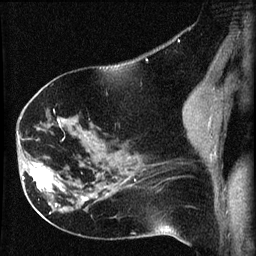
Breast MRI (dynamic contrast-enhanced), one sagittal slice; position 33 of 60 along the scan axis; dynamic contrast-enhanced series, image 2 of 3 at this slice position (ordered by acquisition); 1.5 T; TE 4.2 ms, TR 8.2 ms; 2 mm slice thickness; 256 × 256 image matrix. Female patient, age 63 years.
Structures marked on this image (semi-automatically segmented with operator editing):
- analysis volume of interest (the breast-tissue region the enhancement analysis was run in; not a lesion): bounding box <22,156,64,202> (left, top, right, bottom; pixels)
- tumour enhancement mask (voxels above the 70 % enhancement threshold inside the analysis volume of interest): <22,163,61,192>